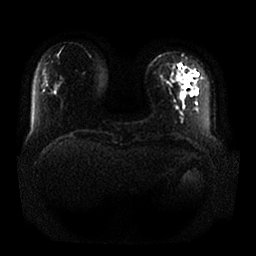
Breast MRI, one axial slice. Slice 4 of 25 in the series (ordered by position). Diffusion-weighted series; image 2 of 4 stored at this slice position (different b-values; order by instance number). 1.5 T. 256 × 256 image matrix, field of view 380 × 380 mm. Female patient.
Structures marked on this image (manually delineated by an expert):
- tumour on diffusion-weighted imaging: bounding box [x1, y1, x2, y2] px = [179, 79, 182, 81]